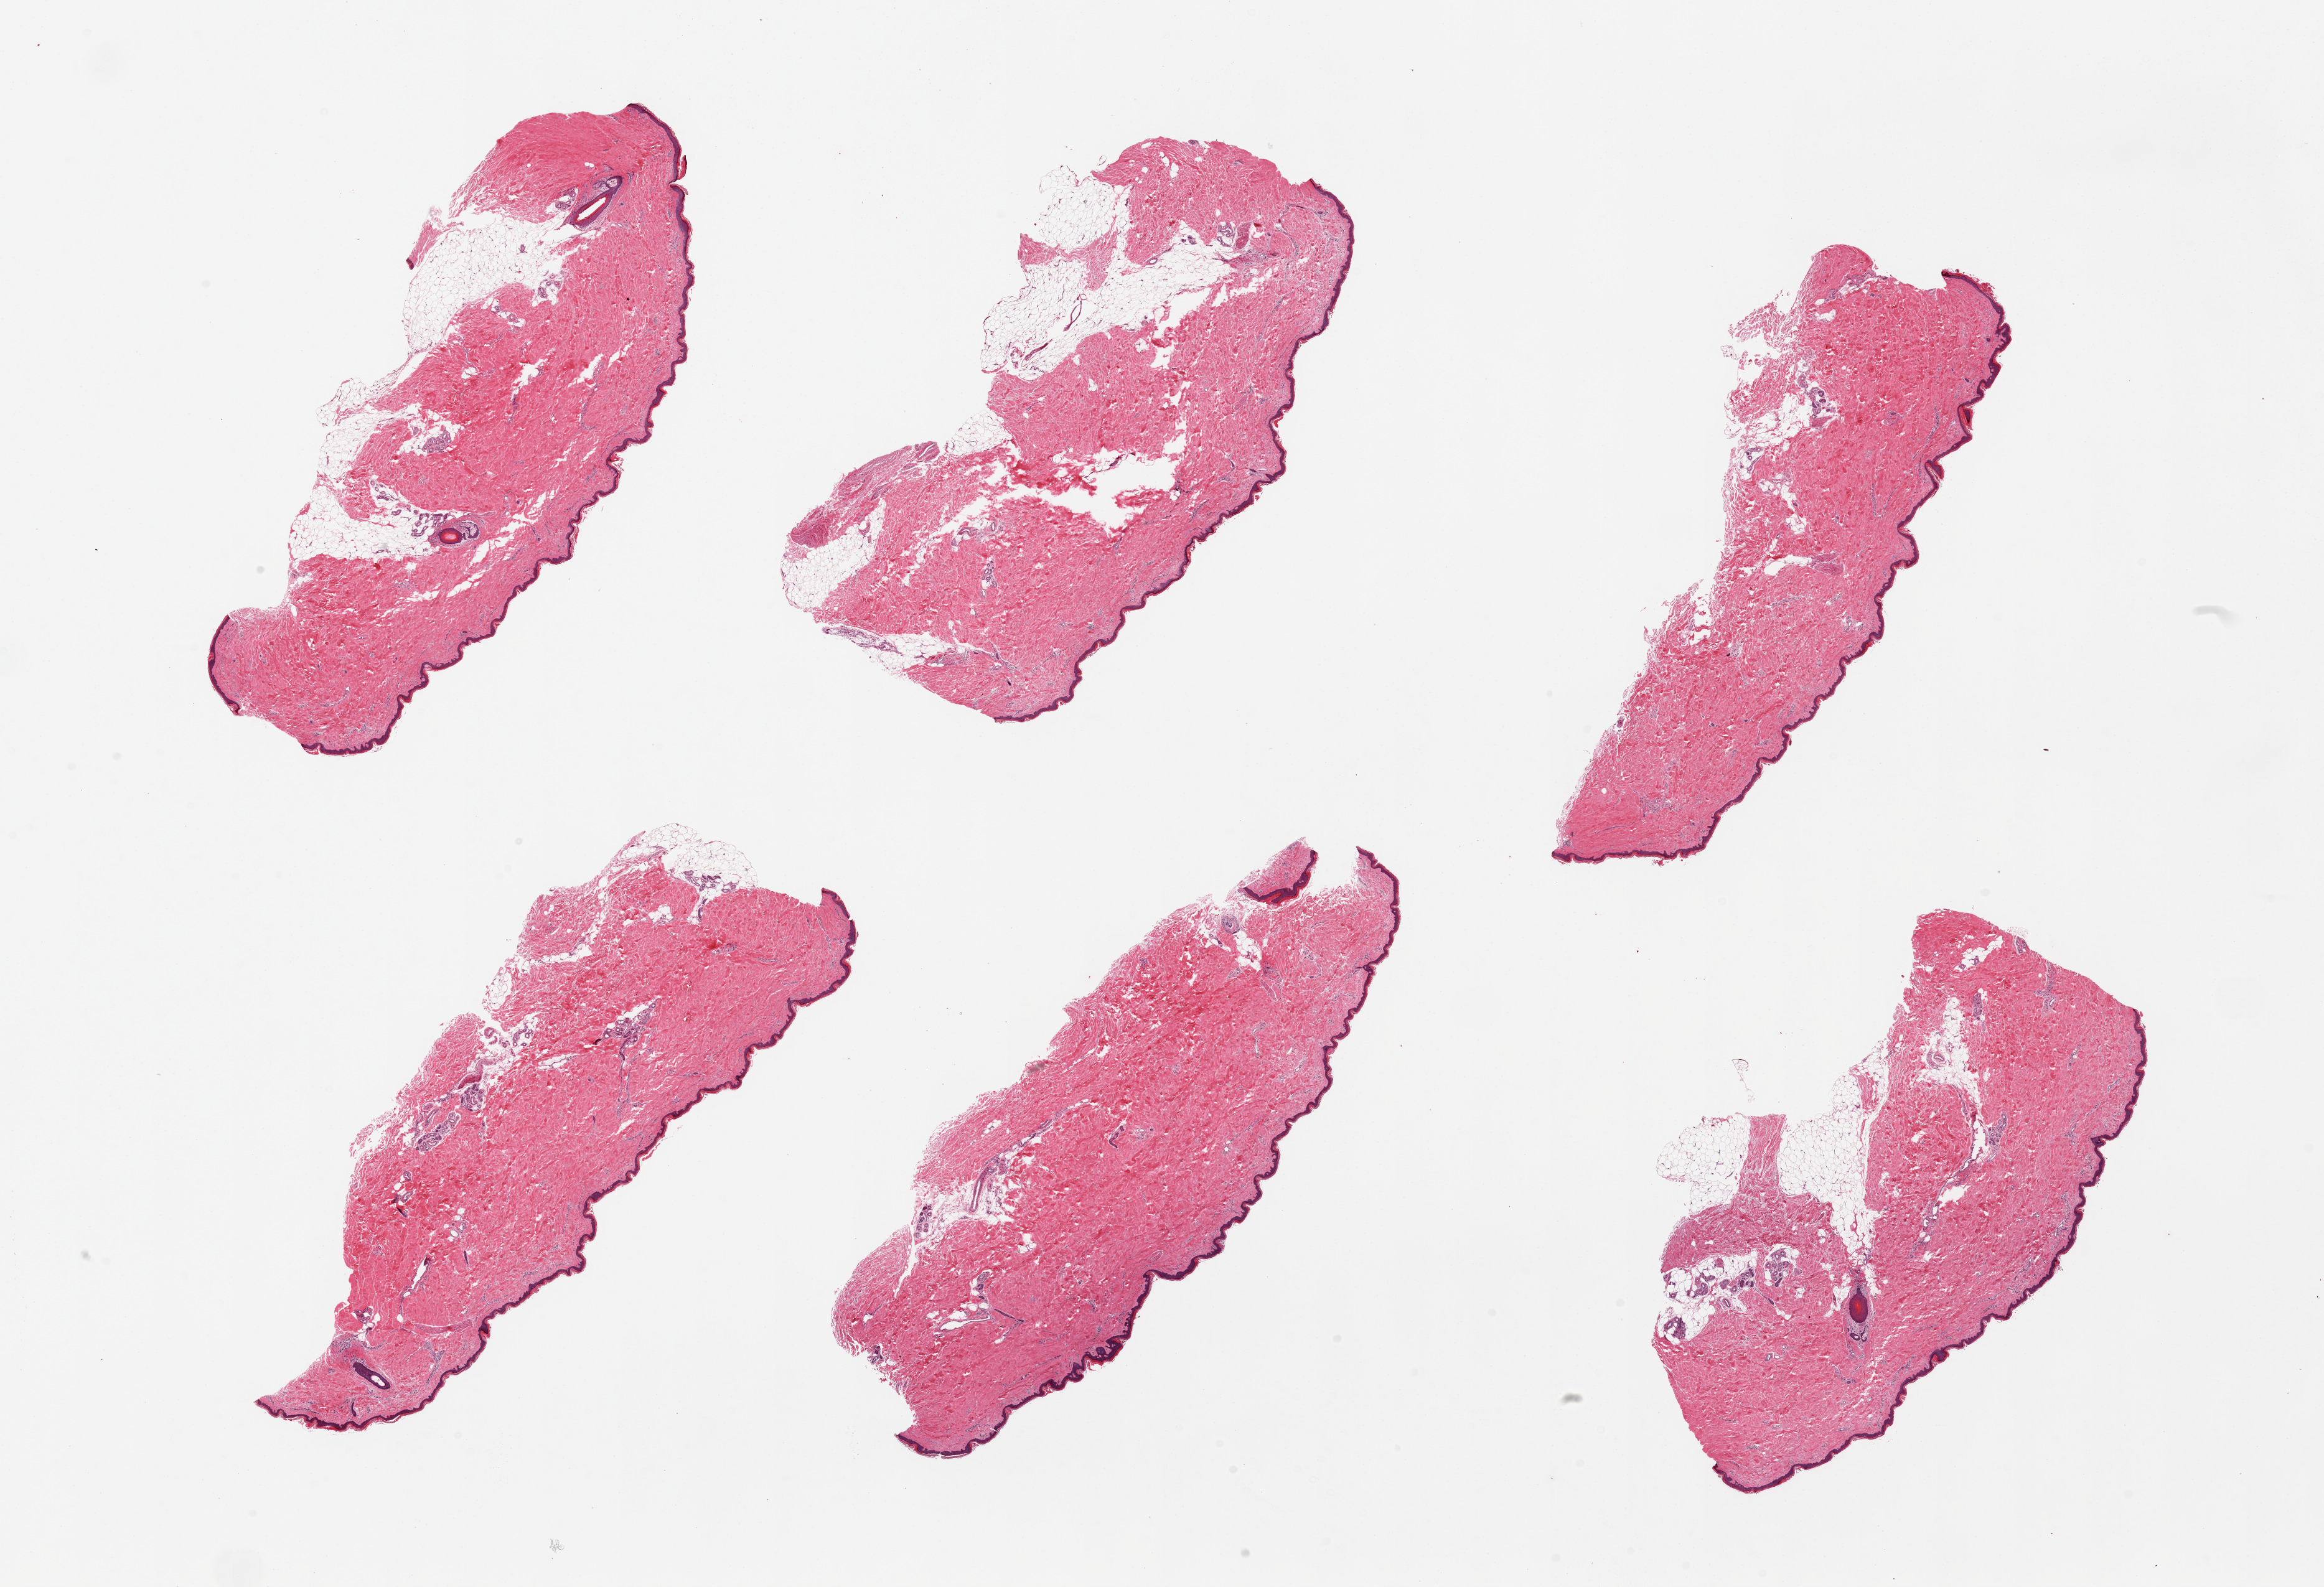
Whole-slide image, hematoxylin and eosin (H&E) stain — whole scanned area (about 29.5 x 20.2 mm, from a 20x scan) shown as a low-resolution overview; PAXgene-fixed paraffin-embedded (PFPE) section; section of skin of lower leg (target tissue); tissue donor sample.
Reviewer comment on this tissue sample: 6 pieces, 3 with up to 10% adipose tissue.